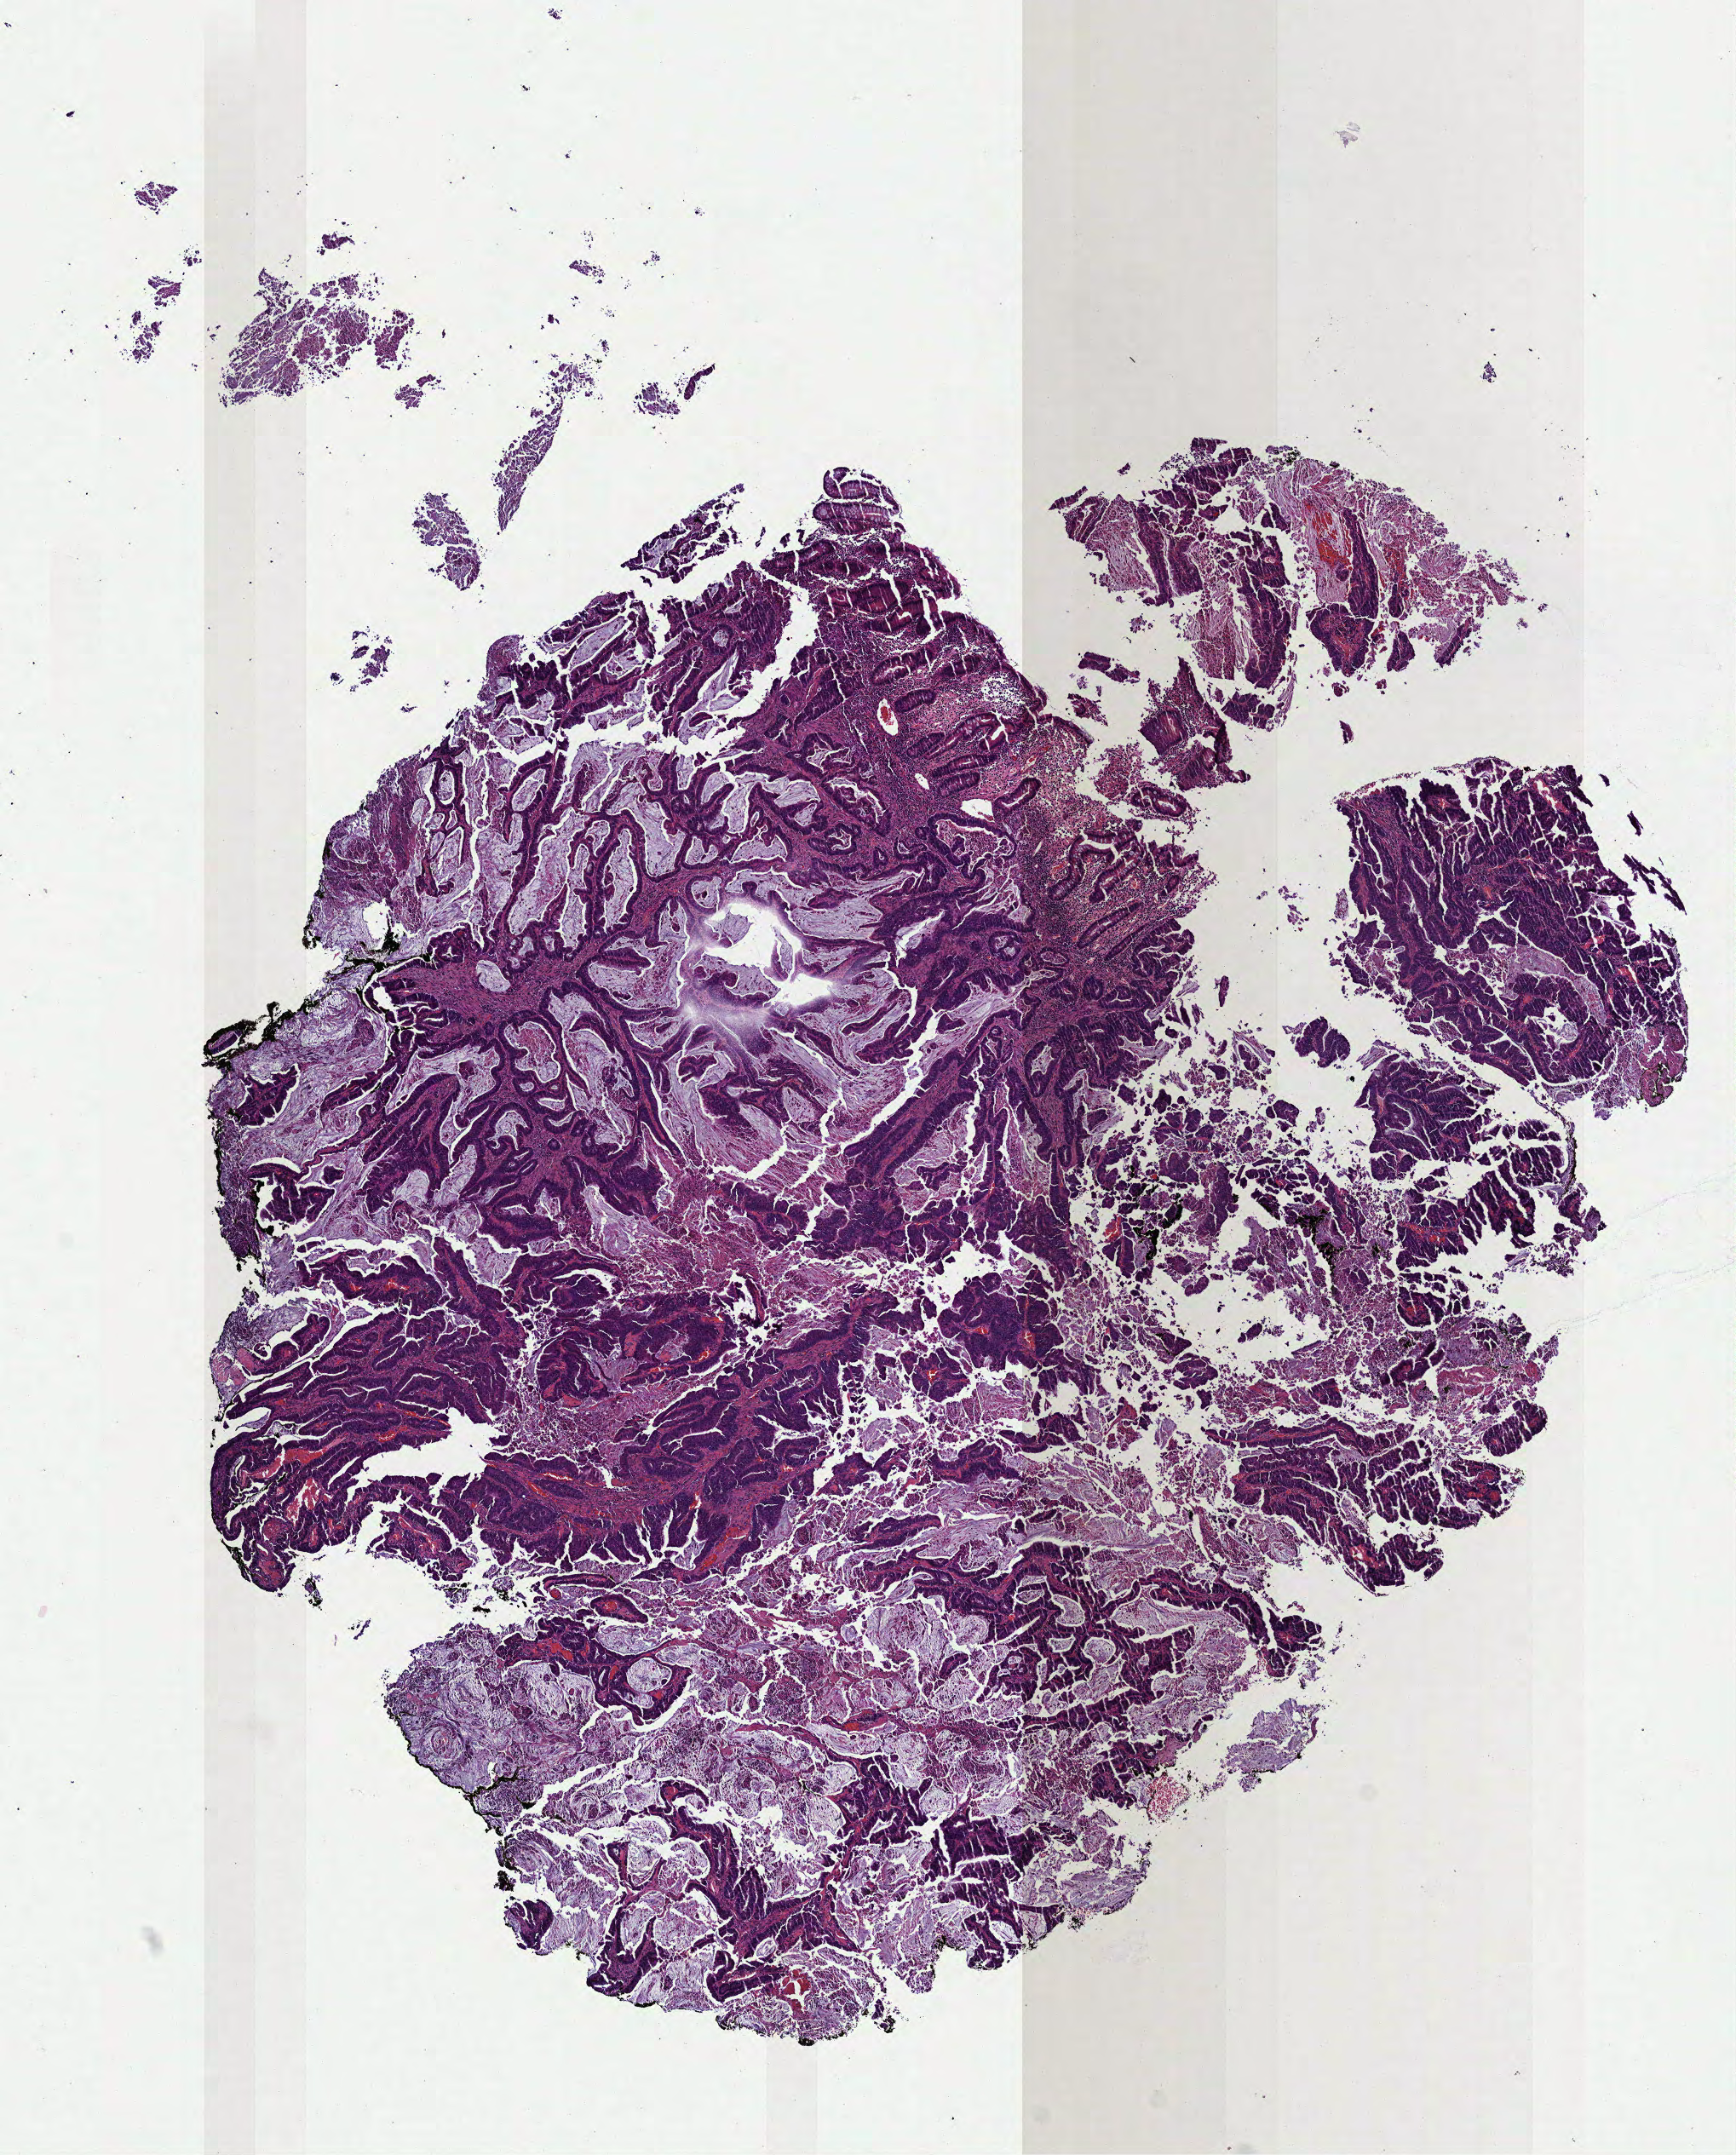
Hematoxylin and eosin (H&E) stained whole-slide image — low-resolution overview of the scanned area, about 8.2 x 10.2 mm (from a 40x scan), FFPE section, sample: primary tumour, colon. Female patient; age at initial diagnosis 74 years.
Histologic diagnosis: Adenocarcinoma, NOS (cecum).